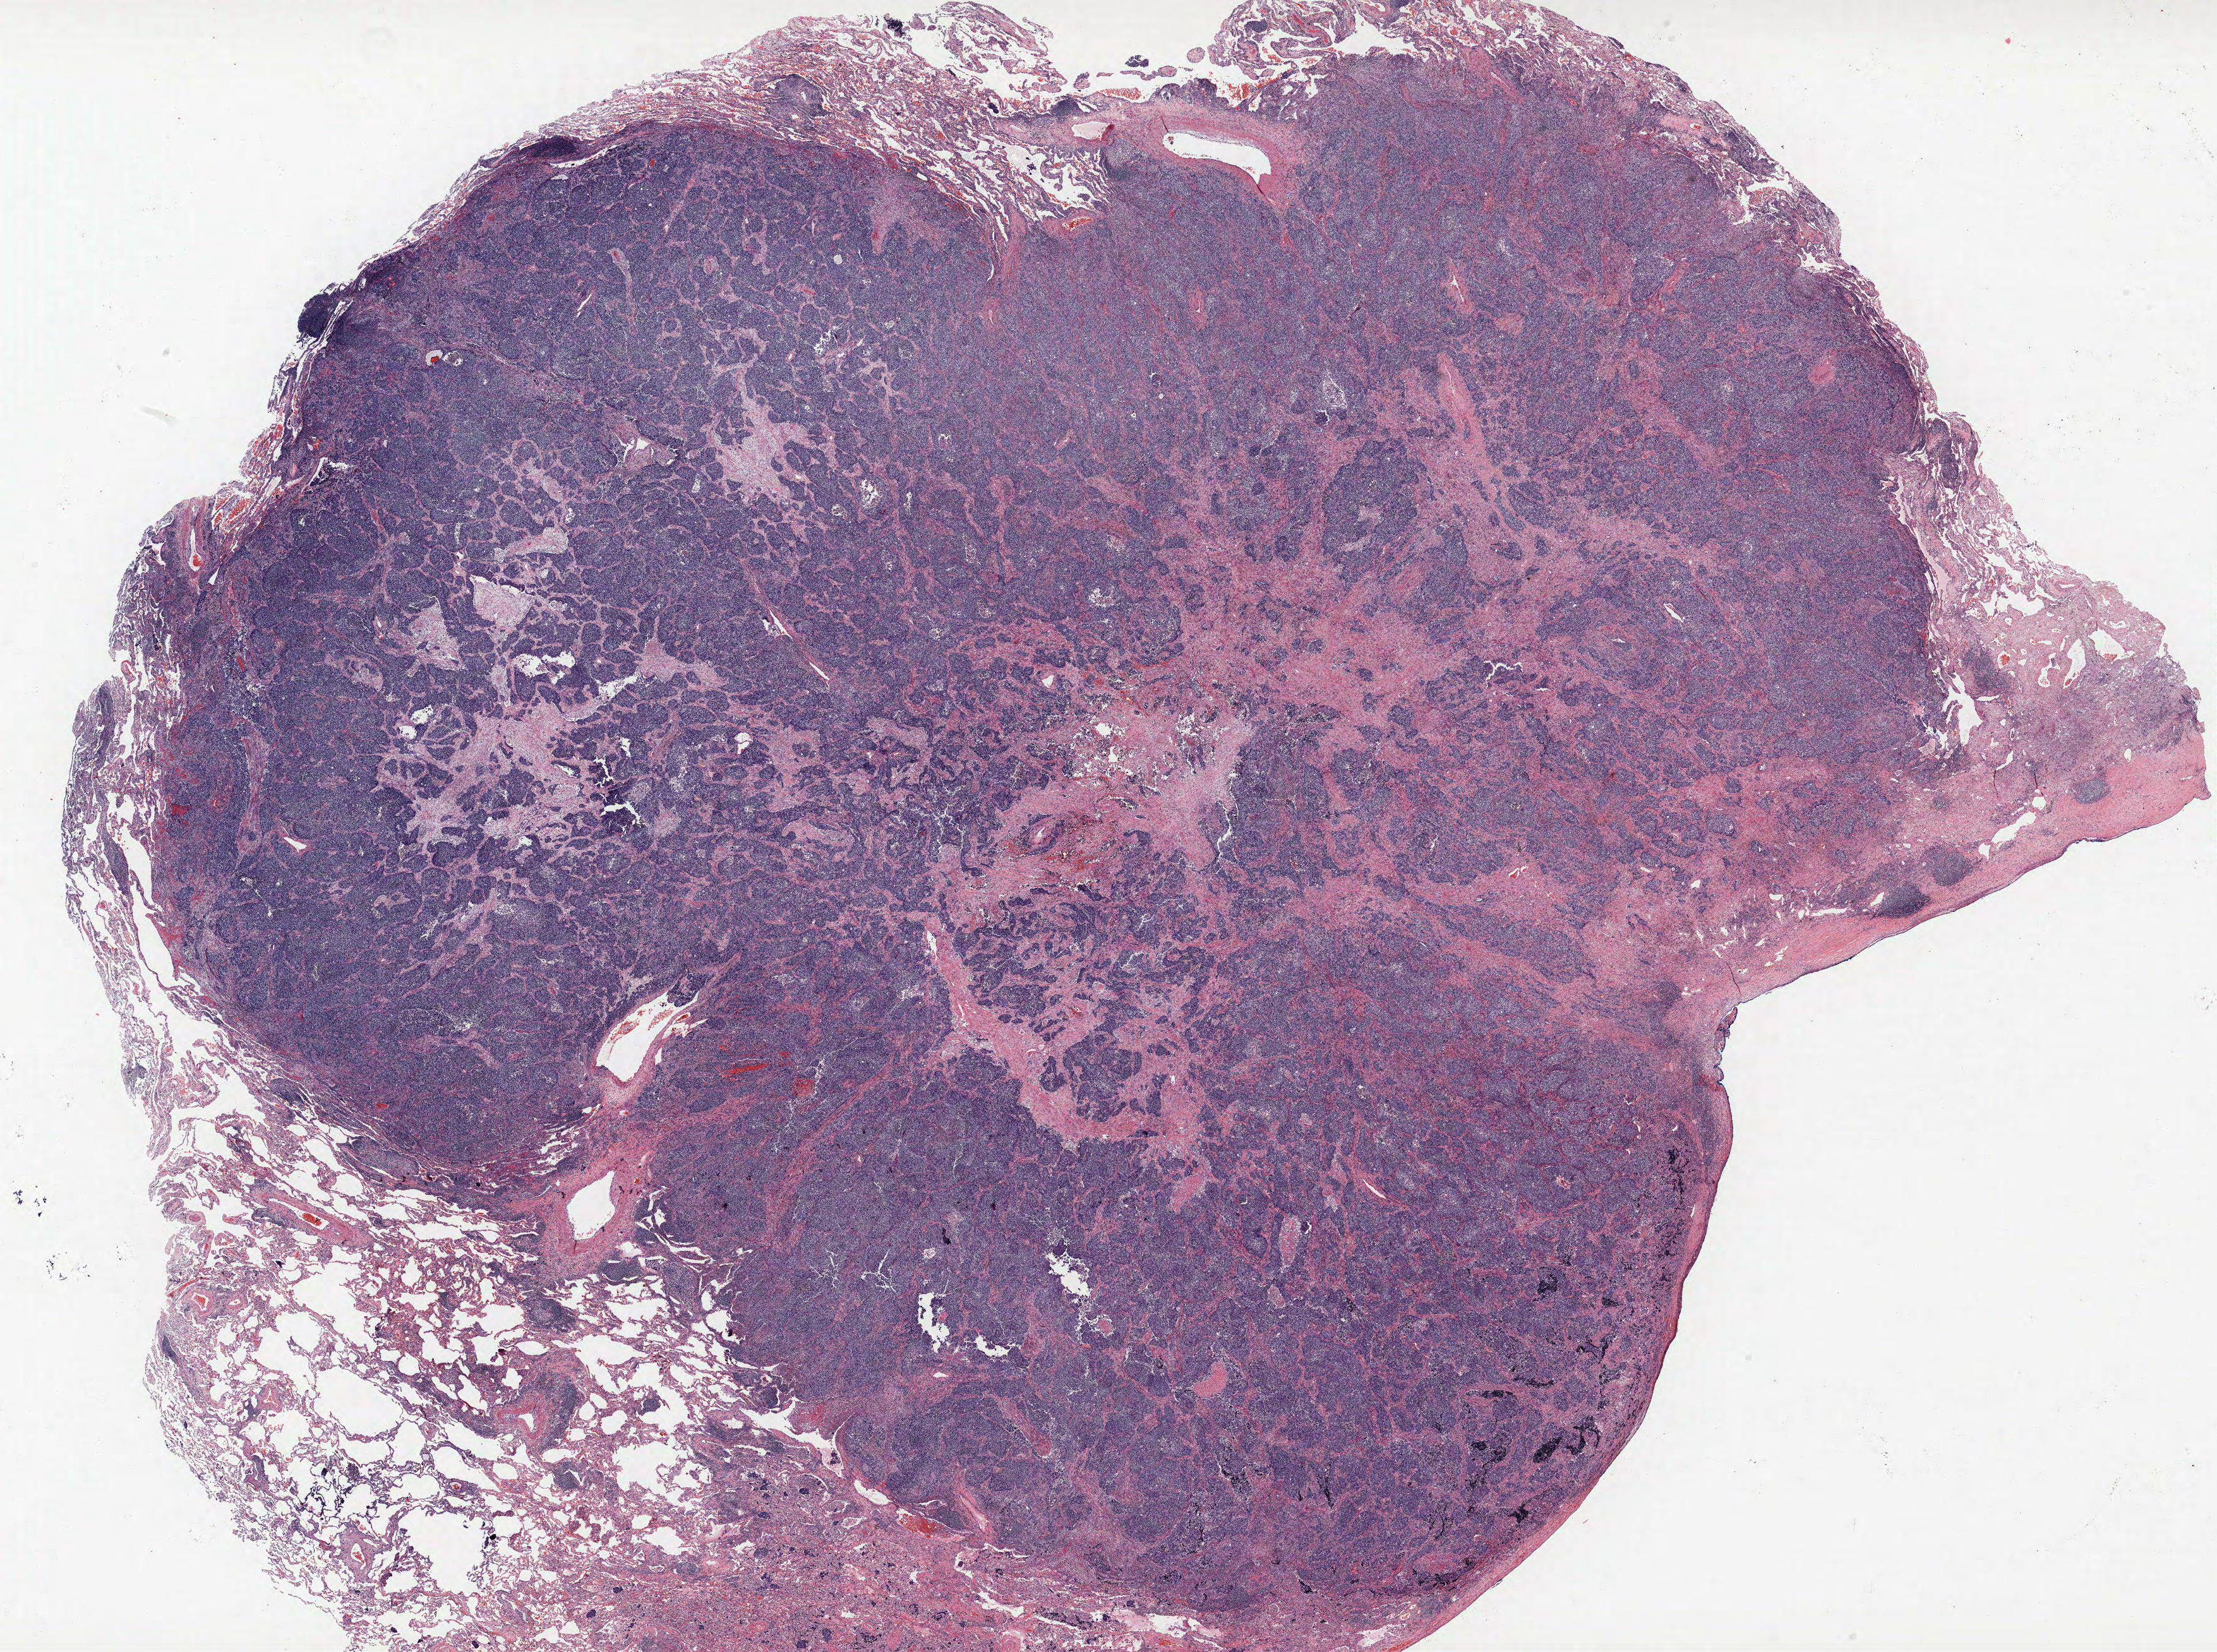
Whole-slide histology image, H&E, a low-resolution overview of the entire scanned area, about 28.1 x 20.9 mm (slide scanned at 40x), FFPE section, lung. Female, age 68 at enrolment. Current smoker at enrolment. Grade: undifferentiated (G4).
ICD-O-3 topography: upper lobe of lung (C34.1). Primary tumour location (clinical record): right upper lobe. Tumour size (pathology): 22 mm. Participant's lung-cancer diagnosis: Large cell neuroendocrine carcinoma (ICD-O-3 8013/3). Stage (AJCC 6th edition): IB.